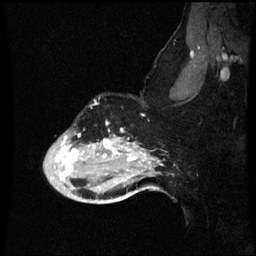
Breast MRI (dynamic contrast-enhanced), one sagittal slice. Position 46 of 60 along the scan axis. Dynamic contrast-enhanced series, image 2 of 3 at this slice position (ordered by acquisition). 1.5 T. TE 4.2 ms, TR 8.9 ms. 2 mm slice thickness. 256 × 256 image matrix, field of view 200 × 200 mm. Patient: female, 49 years. Case-level facts recorded for this patient, not image findings: setting: breast cancer imaged before/during neoadjuvant chemotherapy; receptor status: HR-positive, HER2-negative.
Annotated regions visible in this slice (semi-automatically segmented with operator editing):
- analysis volume of interest (the breast-tissue region the enhancement analysis was run in; not a lesion): box from (x=44, y=124) to (x=159, y=199) px
- tumour enhancement mask (voxels above the 70 % enhancement threshold inside the analysis volume of interest): (x=58, y=130)–(x=147, y=179)